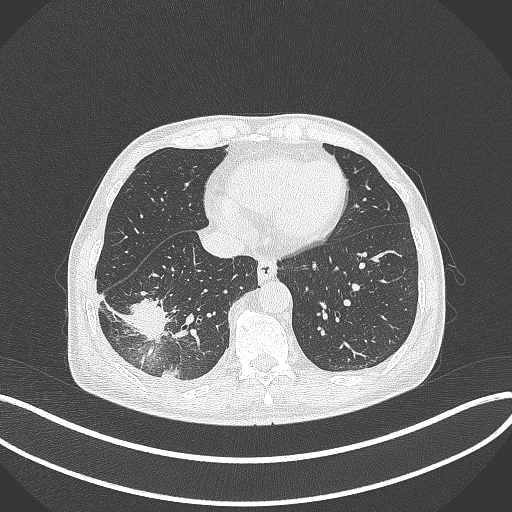
Chest CT, one axial slice; reconstruction kernel B70f; lung window (W 1500 / L -600 HU); 1 mm slice thickness; 512 × 512 image matrix, field of view 400 × 400 mm. Patient: male, 64 years. Case-level facts recorded for this patient, not image findings: clinical TNM (as recorded): T3 N0 M0.
Outlined on this slice (rectangle marked by the reading radiologist):
- lung tumour (recorded histology: adenocarcinoma): bounding box (x1, y1, x2, y2) in pixels: (120, 293, 173, 349)